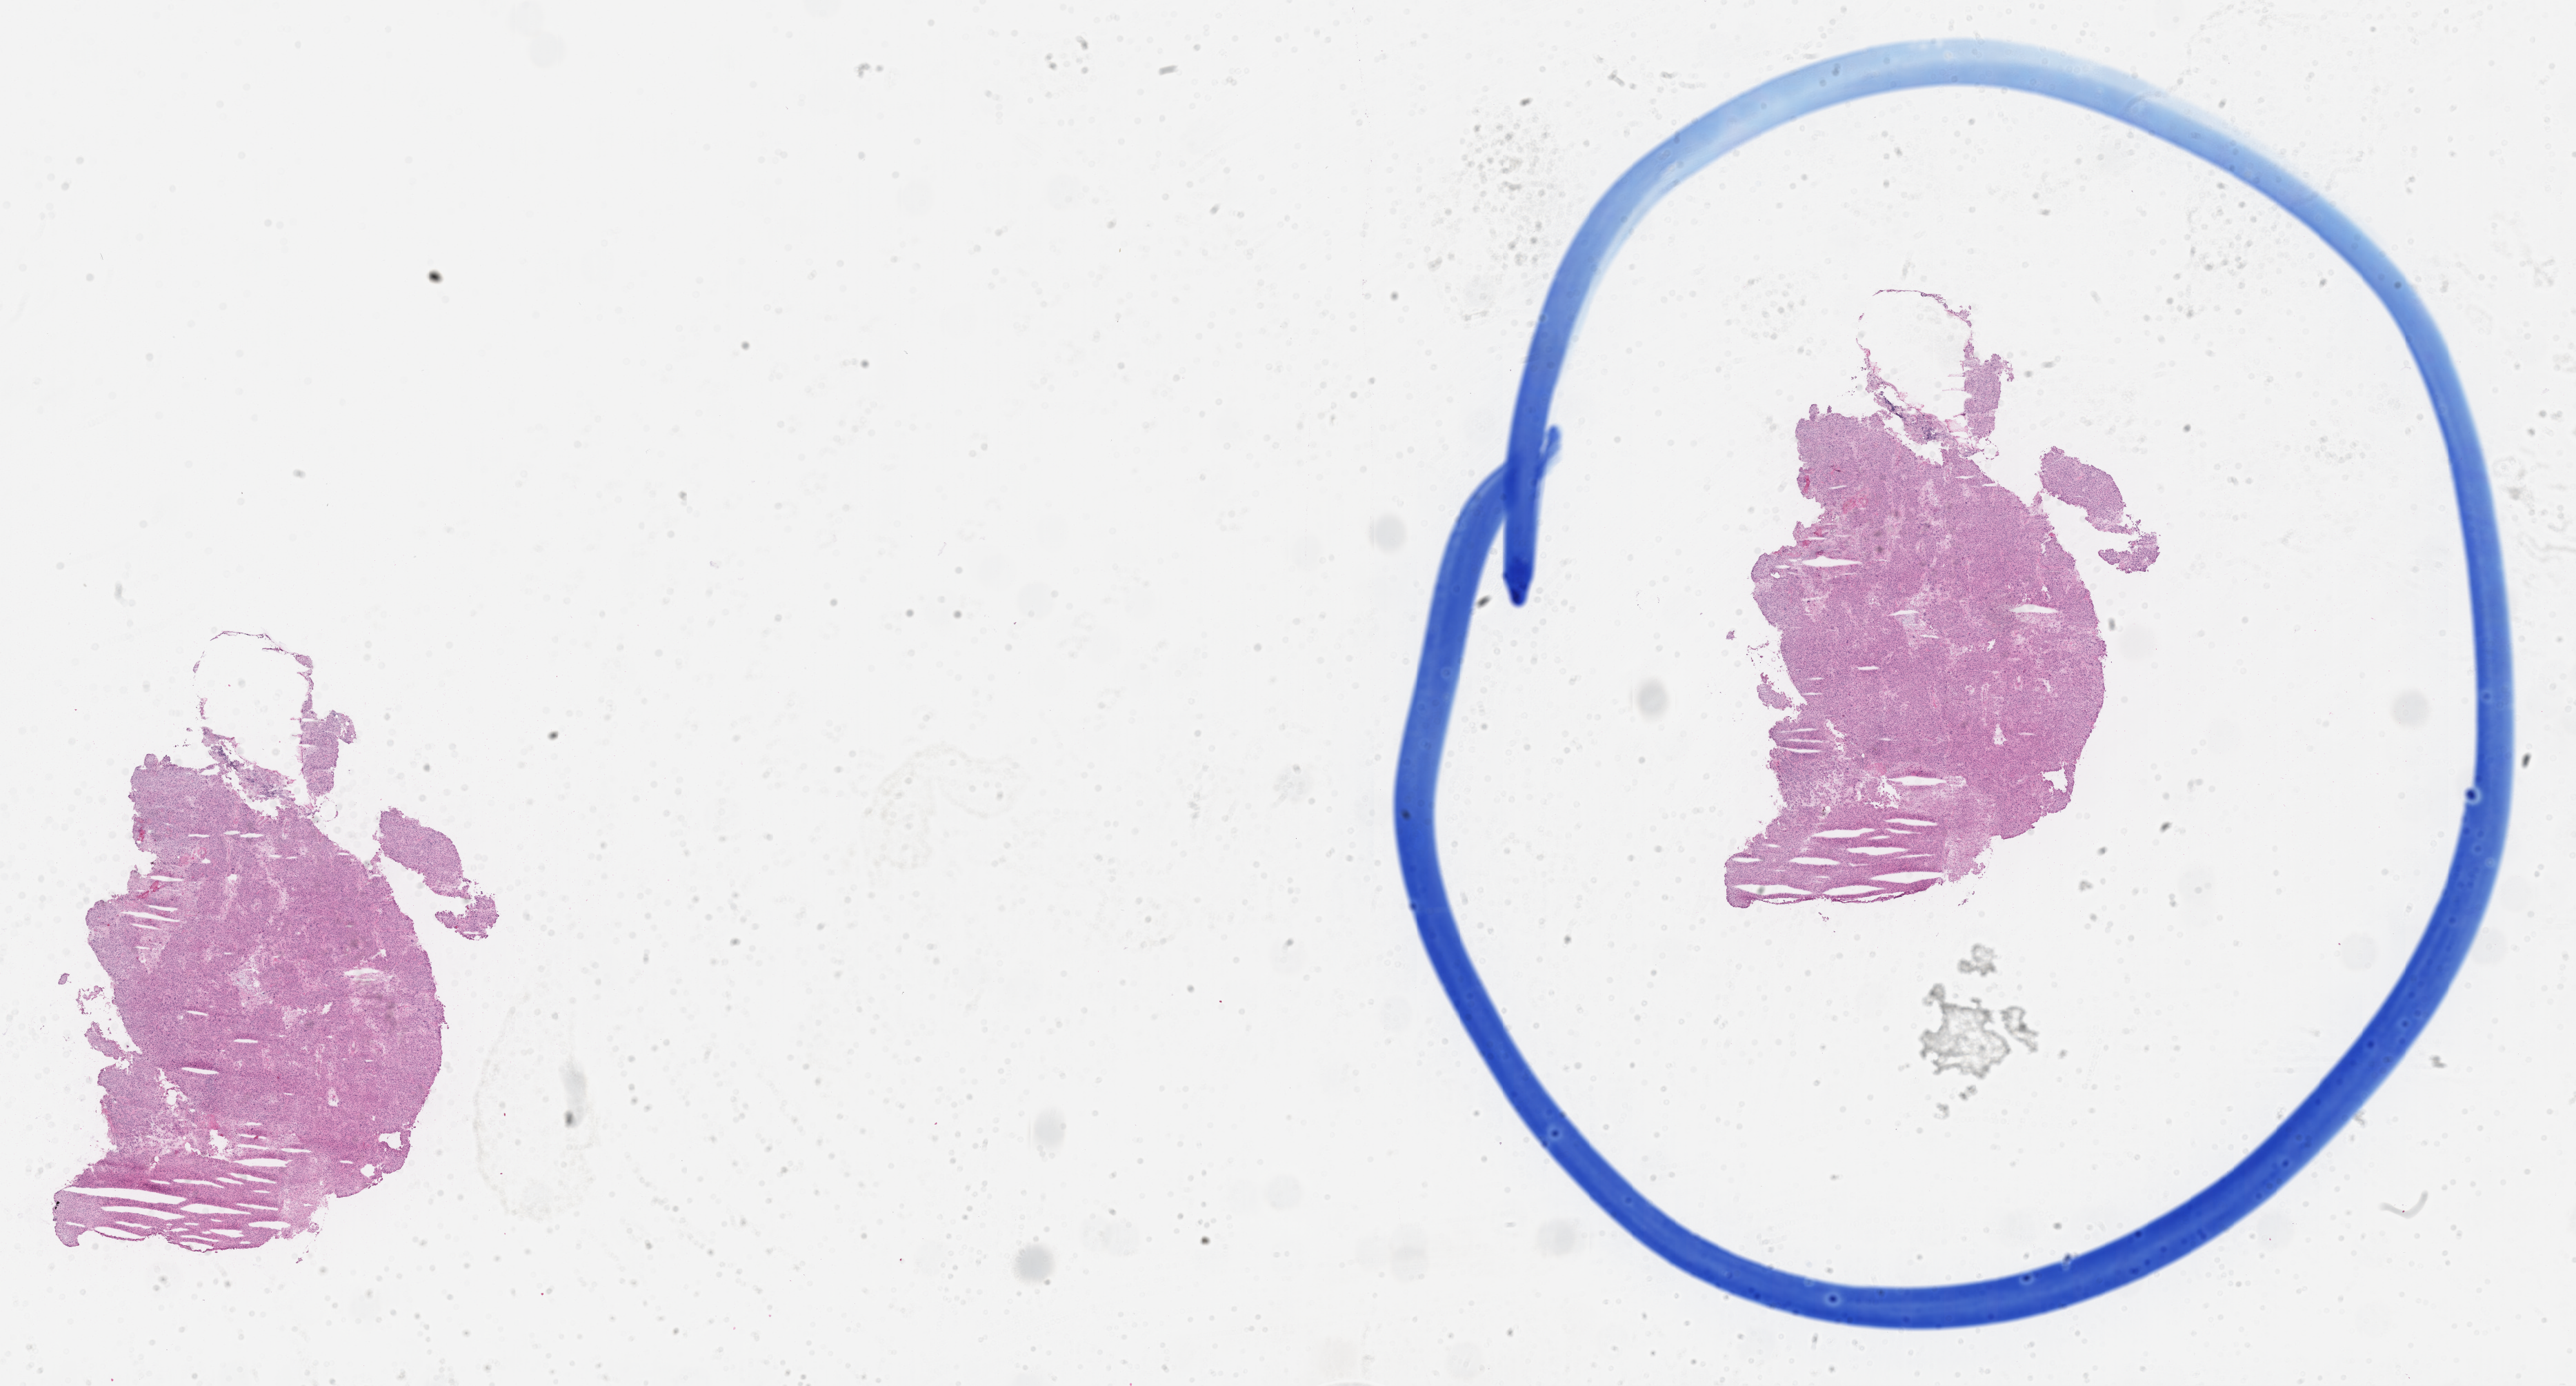
Whole-slide image, haematoxylin and eosin stain, shown as a low-resolution overview of the whole scanned area (about 30.1 x 16.2 mm); cryosection; specimen: primary tumor; site: breast (right). Female, age 38 years at initial diagnosis. Slide review estimates, as recorded: tumor cells 85%, tumor nuclei 85%, stromal cells 10%, necrosis 0%, normal cells 5%. Inflammatory infiltration, as recorded: lymphocyte infiltration 5%, monocyte infiltration 0%, neutrophil infiltration 0%.
- histologic diagnosis: Infiltrating duct carcinoma, NOS